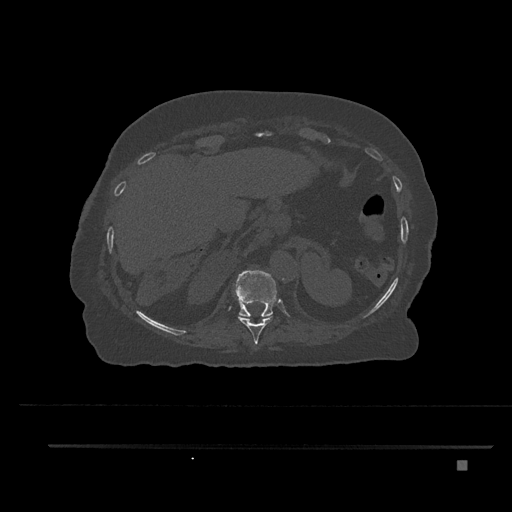
CT including the spine, one axial slice. Position 334 of 797 along the scan axis. Reconstruction kernel Br40s/3. Bone window (W 1800 / L 400 HU). 0.5 mm slice thickness. 512 × 512 image matrix, field of view 437 × 437 mm. Patient: female, 76 years. Case-level facts recorded for this patient, not image findings: primary cancer: lung.
Structures marked on this image (semi-automatic segmentation, software-assisted and operator-edited):
- T10 vertebra: box from (x=238, y=315) to (x=273, y=344) px
- T11 vertebra: (x=233, y=270)–(x=277, y=317)